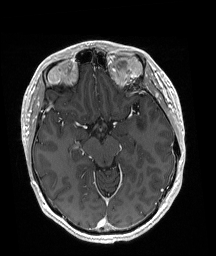
Brain MRI from a brain-tumour surgery series, one axial slice. Position 115 of 192 along the scan axis. T1-weighted post-contrast. 1 mm slice thickness. 216 × 256 image matrix, field of view 211 × 250 mm. From the clinical record (not read from this slice): histopathology: Astrocytoma; WHO grade: 3; IDH mutation: yes.
Annotated regions visible in this slice (expert manual segmentation):
- tumour: bounding box [x1, y1, x2, y2] px = [136, 118, 145, 136]